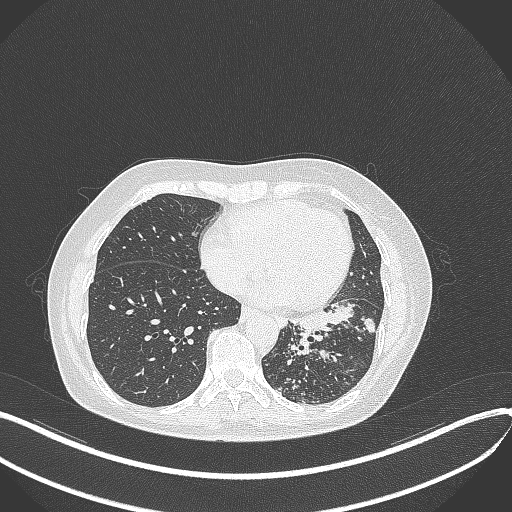
Chest CT, one axial slice. 100 kVp. Lung window (W 1500 / L -600 HU). 1 mm slice thickness. 512 × 512 image matrix. Female patient, age 63 years. Case-level facts recorded for this patient, not image findings: clinical TNM (as recorded): T1b N0 M0.
Annotated regions visible in this slice (rectangle marked by the reading radiologist):
- lung tumour (recorded histology: adenocarcinoma): bounding box (x1, y1, x2, y2) in pixels: (286, 298, 377, 335)